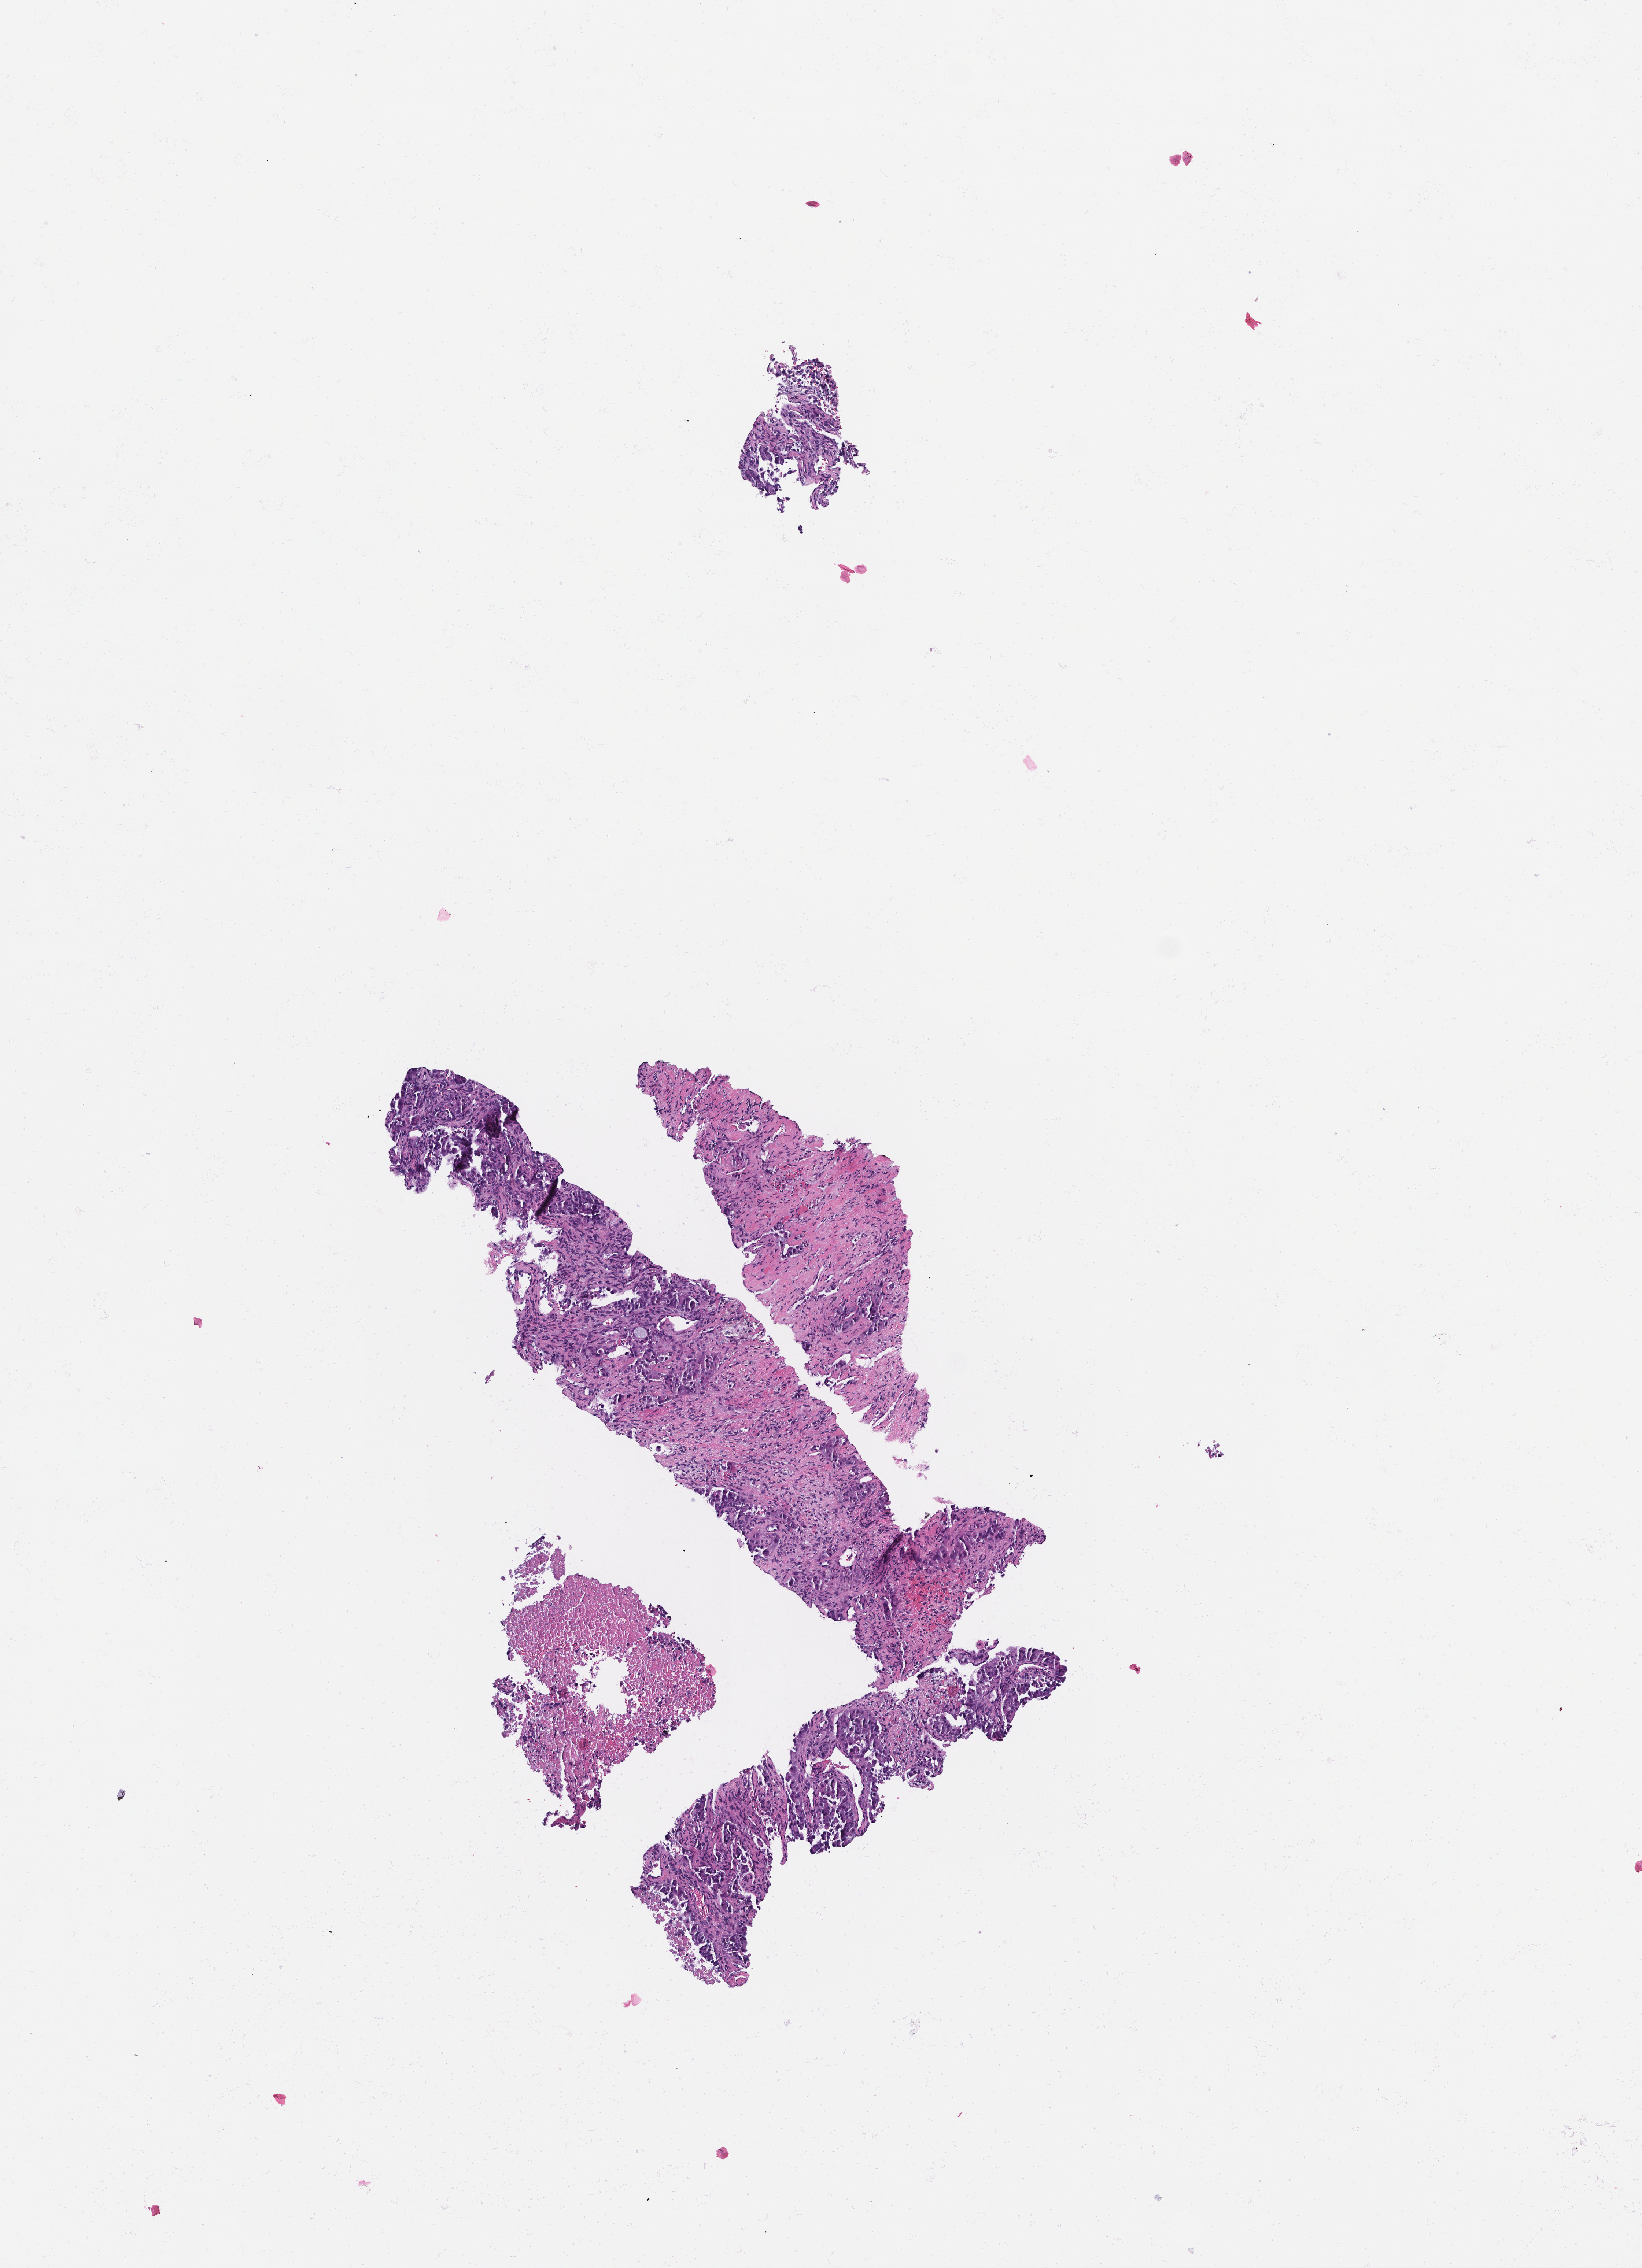
Haematoxylin and eosin whole-slide image, whole scanned area (about 4.5 x 6.2 mm) shown as a low-resolution overview. Formalin-fixed paraffin-embedded section. Patient: male.
This section: metastatic tumor tissue. Primary diagnosis of the patient: Non-Small Cell Lung Carcinoma.